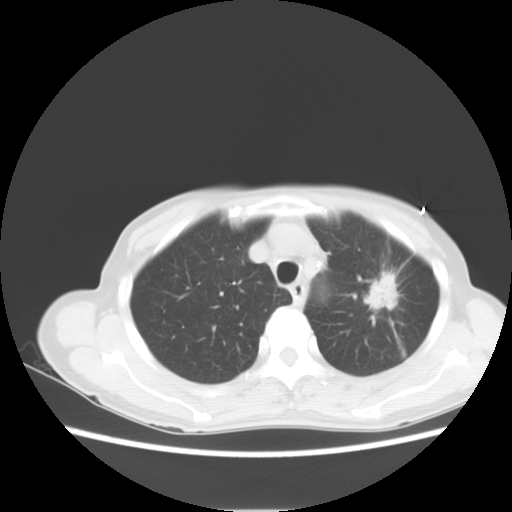
Chest CT, one axial slice. Slice 8 of 14 in the series (ordered by position). 120 kVp. Lung window (W 1500 / L -600 HU). 5 mm slice thickness. 512 × 512 image matrix, field of view 350 × 350 mm. Patient: female, 71 years. Case-level facts recorded for this patient, not image findings: clinical TNM (as recorded): T2 N0 M0.
Structures marked on this image (bounding box drawn by a radiologist):
- lung tumour (recorded histology: adenocarcinoma): box from (x=366, y=269) to (x=401, y=314) px